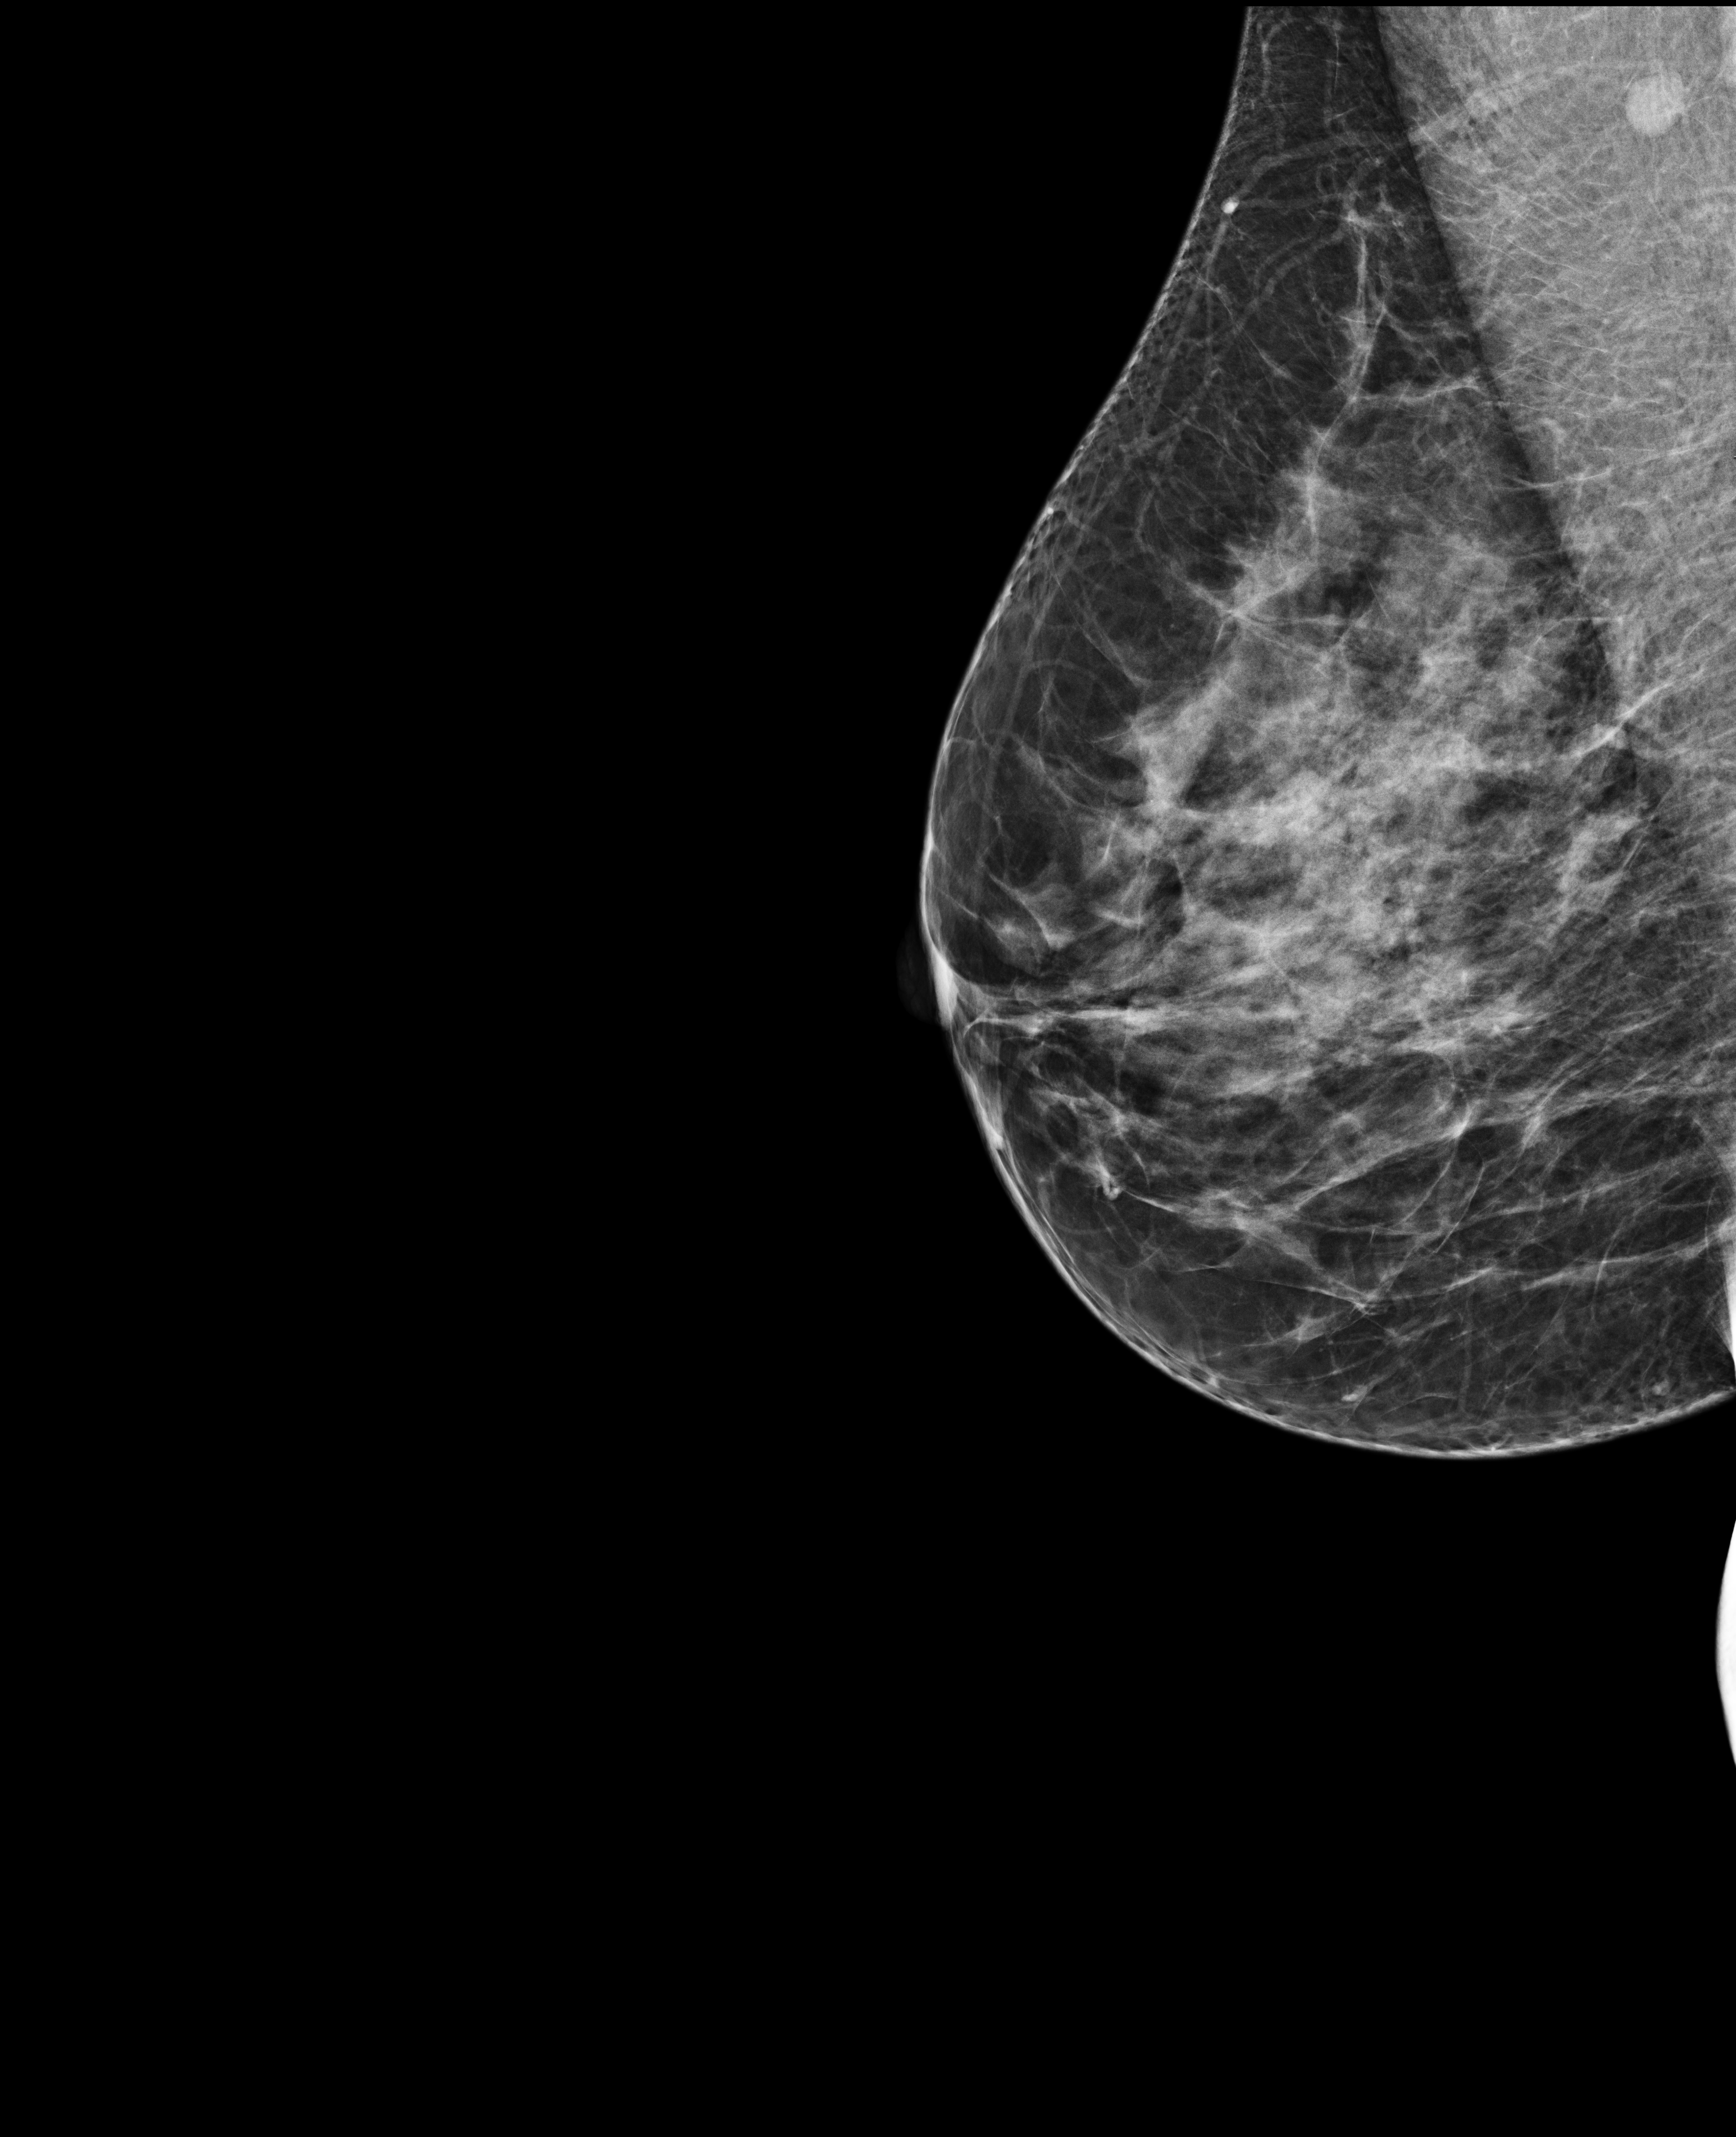
Full-field digital mammogram (FFDM); left breast; MLO view; screening examination; compressed breast thickness 60 mm. Patient aged 48 years (female).
BI-RADS breast density category at the screening exam (both breasts, scale 1–4): 3. Final BI-RADS category for the screening round (tomosynthesis exam, both breasts): category 1. Recall: no recall after this screen.